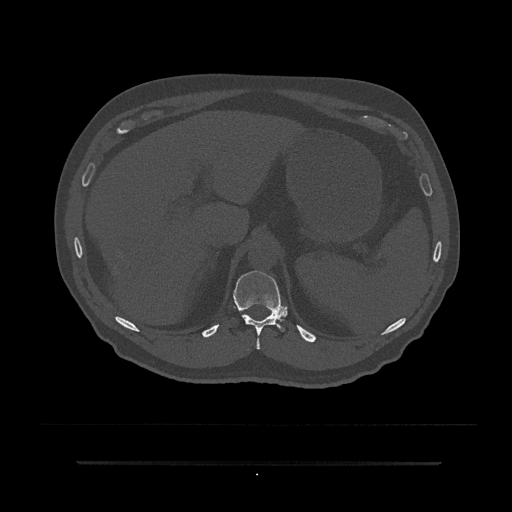
CT including the spine, one axial slice; reconstruction kernel Br40s/3; bone window (W 1800 / L 400 HU); 0.5 mm slice thickness; 512 × 512 image matrix, field of view 464 × 464 mm. Male patient, age 59 years. Case-level facts recorded for this patient, not image findings: primary cancer: bile ducts; vertebrae with lytic lesions (as recorded): T10.
Structures marked on this image (semi-automatic segmentation, software-assisted and operator-edited):
- T11 vertebra: bounding box [x1, y1, x2, y2] px = [233, 271, 285, 349]